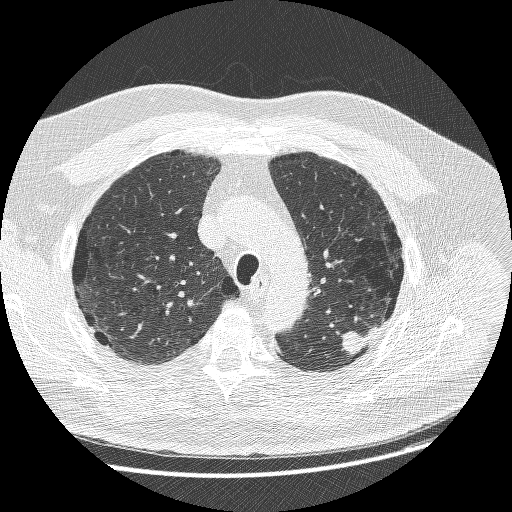
Chest CT (low-dose screening protocol), one axial image; baseline annual screen; lung window (W 1500 / L -600 HU); 1.25 mm slice thickness; lung (sharp) reconstruction kernel (BONE); slice 200 of 258 in the series. Male participant, aged 68 years at enrolment. Former smoker at enrolment.
Lesion marked by an expert reader, bounding box [x1, y1, x2, y2] px = [333, 315, 390, 363]. Reader record for this screening exam (exam-level; its link to the box is not recorded): non-calcified nodule or mass ≥4 mm, left upper lobe, 15 × 14 mm, smooth margins, soft tissue attenuation. Participant outcome: lung cancer diagnosed 19 days after this screen — adenosquamous carcinoma, left upper lobe, poorly differentiated (G3), stage IIIB (AJCC 6th edition), 32 mm at pathology.